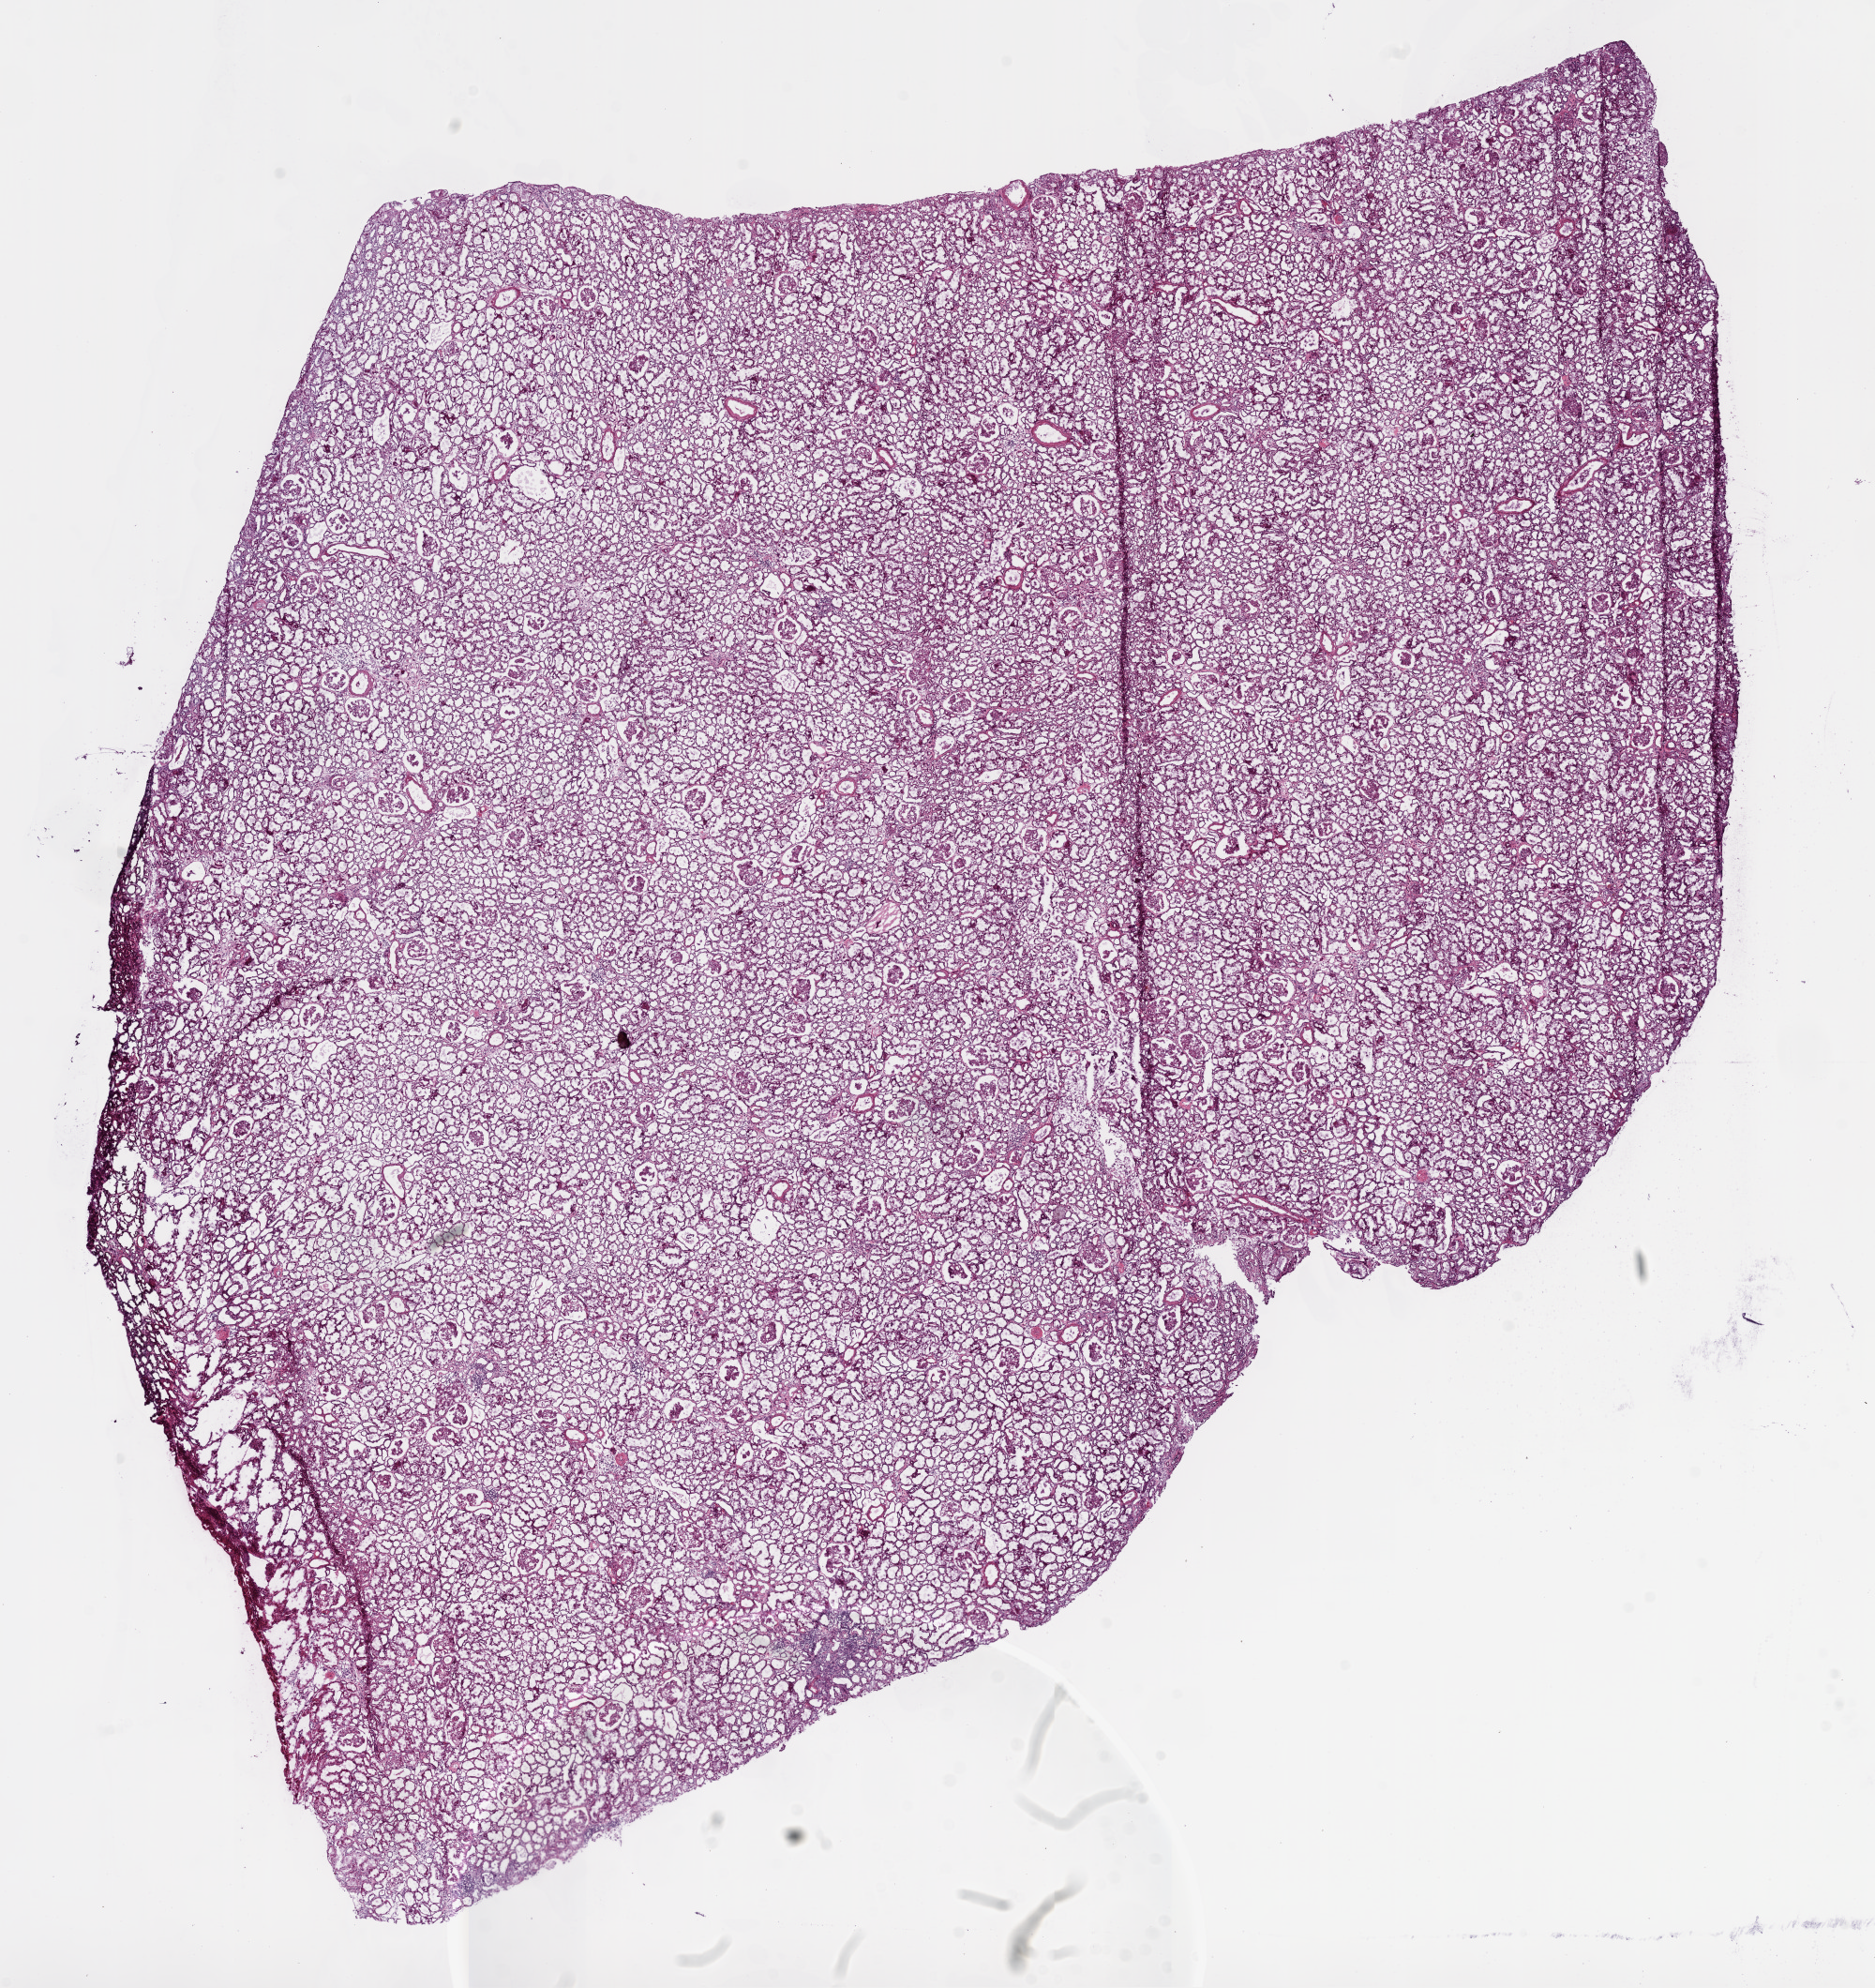
Whole-slide histology image, Hematoxylin and eosin (H&E) stained — shown as a low-resolution overview of the whole scanned area (about 16.0 x 17.0 mm), frozen section, solid tissue normal (non-tumour tissue) sample from the kidney. Female patient; age at initial diagnosis 75 years.
This section: solid tissue normal sample (biorepository sample class). Patient diagnosis: Clear cell adenocarcinoma, NOS.